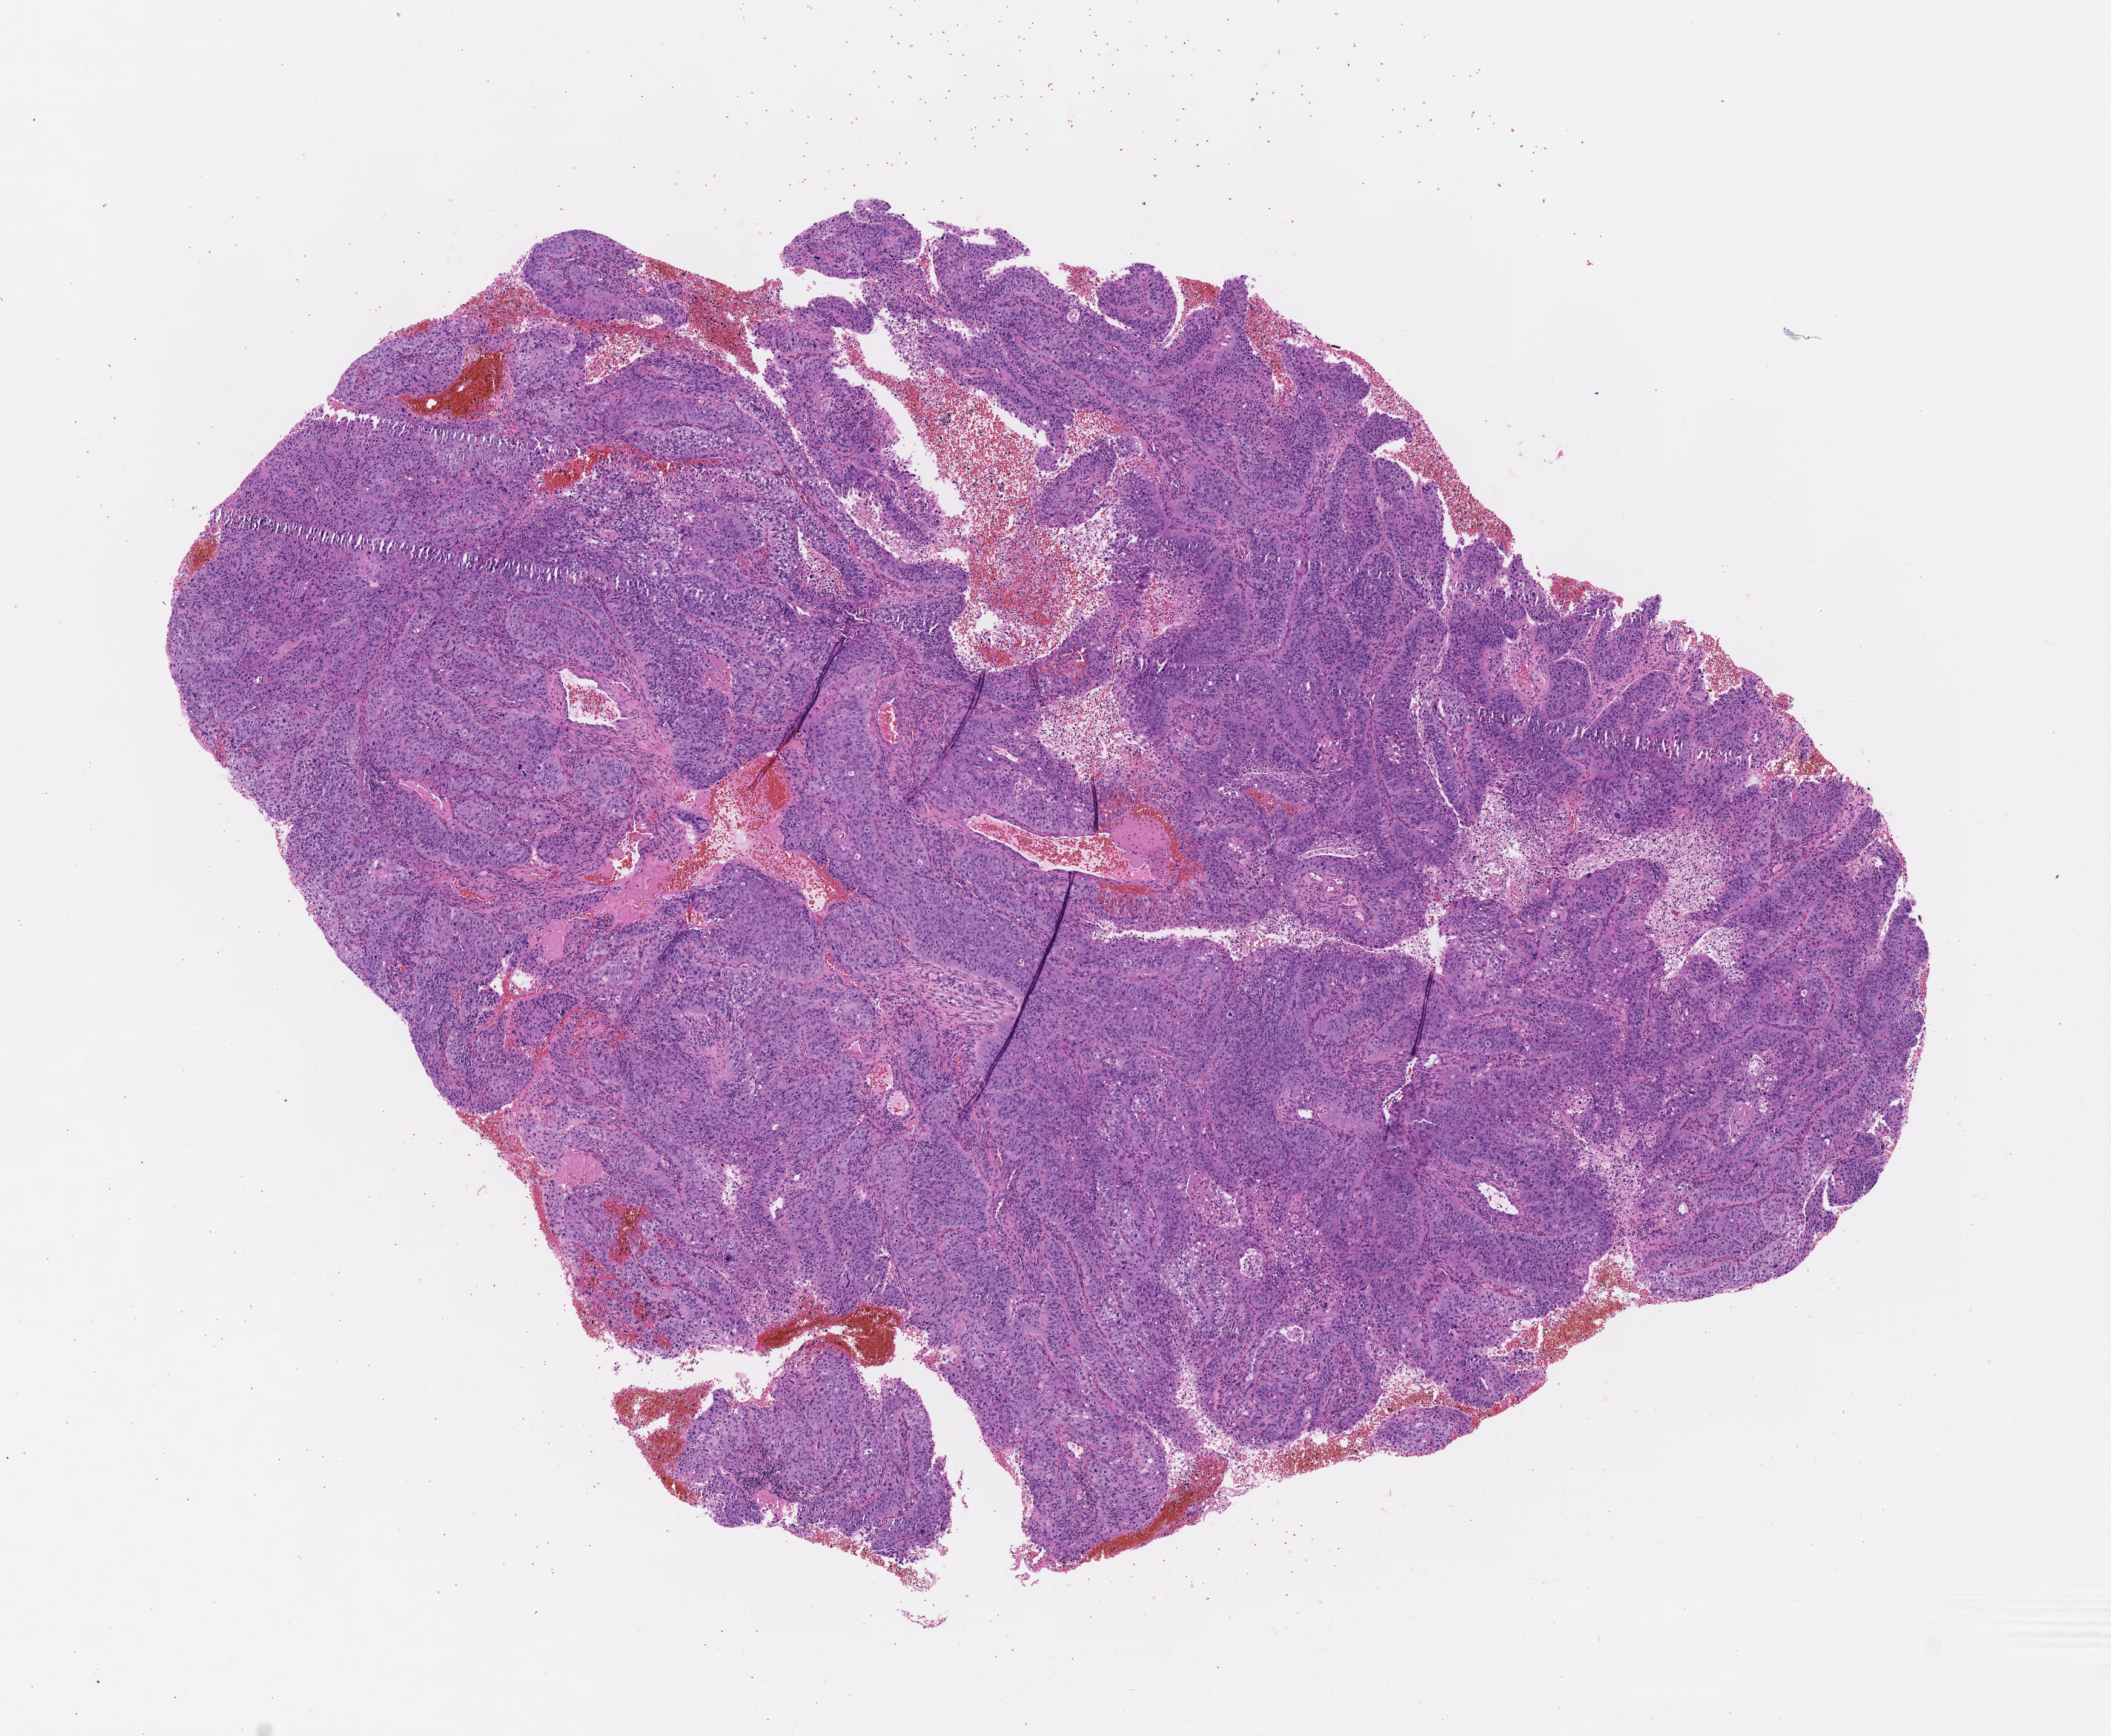
Whole-slide image, haematoxylin and eosin stain, a low-resolution overview of the entire scanned area, about 7.0 x 5.8 mm; specimen: tumor tissue; anatomic site: cervix. Patient: female, 40 years old.
* diagnosis: Squamous cell carcinoma, large cell, nonkeratinizing, NOS